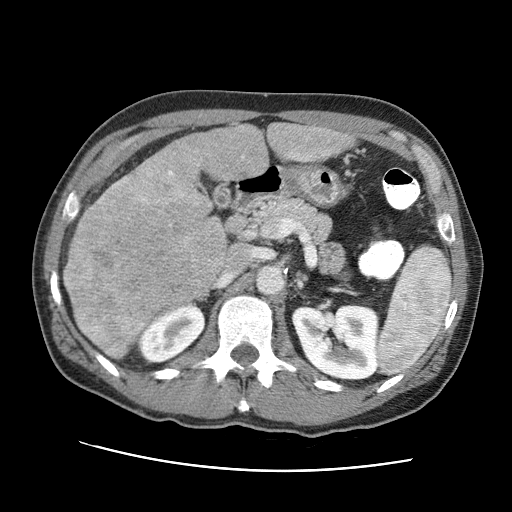
Contrast-enhanced abdominal CT (liver protocol), one axial slice; slice 39 of 95 in the series (ordered by position); one of 2 acquisitions stored at this slice position; soft-tissue window (W 400 / L 40 HU); 2.5 mm slice thickness; 512 × 512 image matrix, field of view 360 × 360 mm. Case-level facts recorded for this patient, not image findings: diagnosis: hepatocellular carcinoma (patient treated with transarterial chemoembolisation; whether this scan precedes or follows treatment is not stated here); TNM stage (as recorded): Stage-IVA; Child-Pugh class: A; tumour nodularity: multinodular.
Structures marked on this image (semi-automatic segmentation, software-assisted and operator-edited):
- liver parenchyma outside the tumour (the mass and vessels are separate outlines, so this box may not span the whole liver): bounding box (x1, y1, x2, y2) in pixels: (62, 122, 352, 309)
- mass: (63, 153, 227, 358)
- liver vessels: (196, 126, 330, 161)